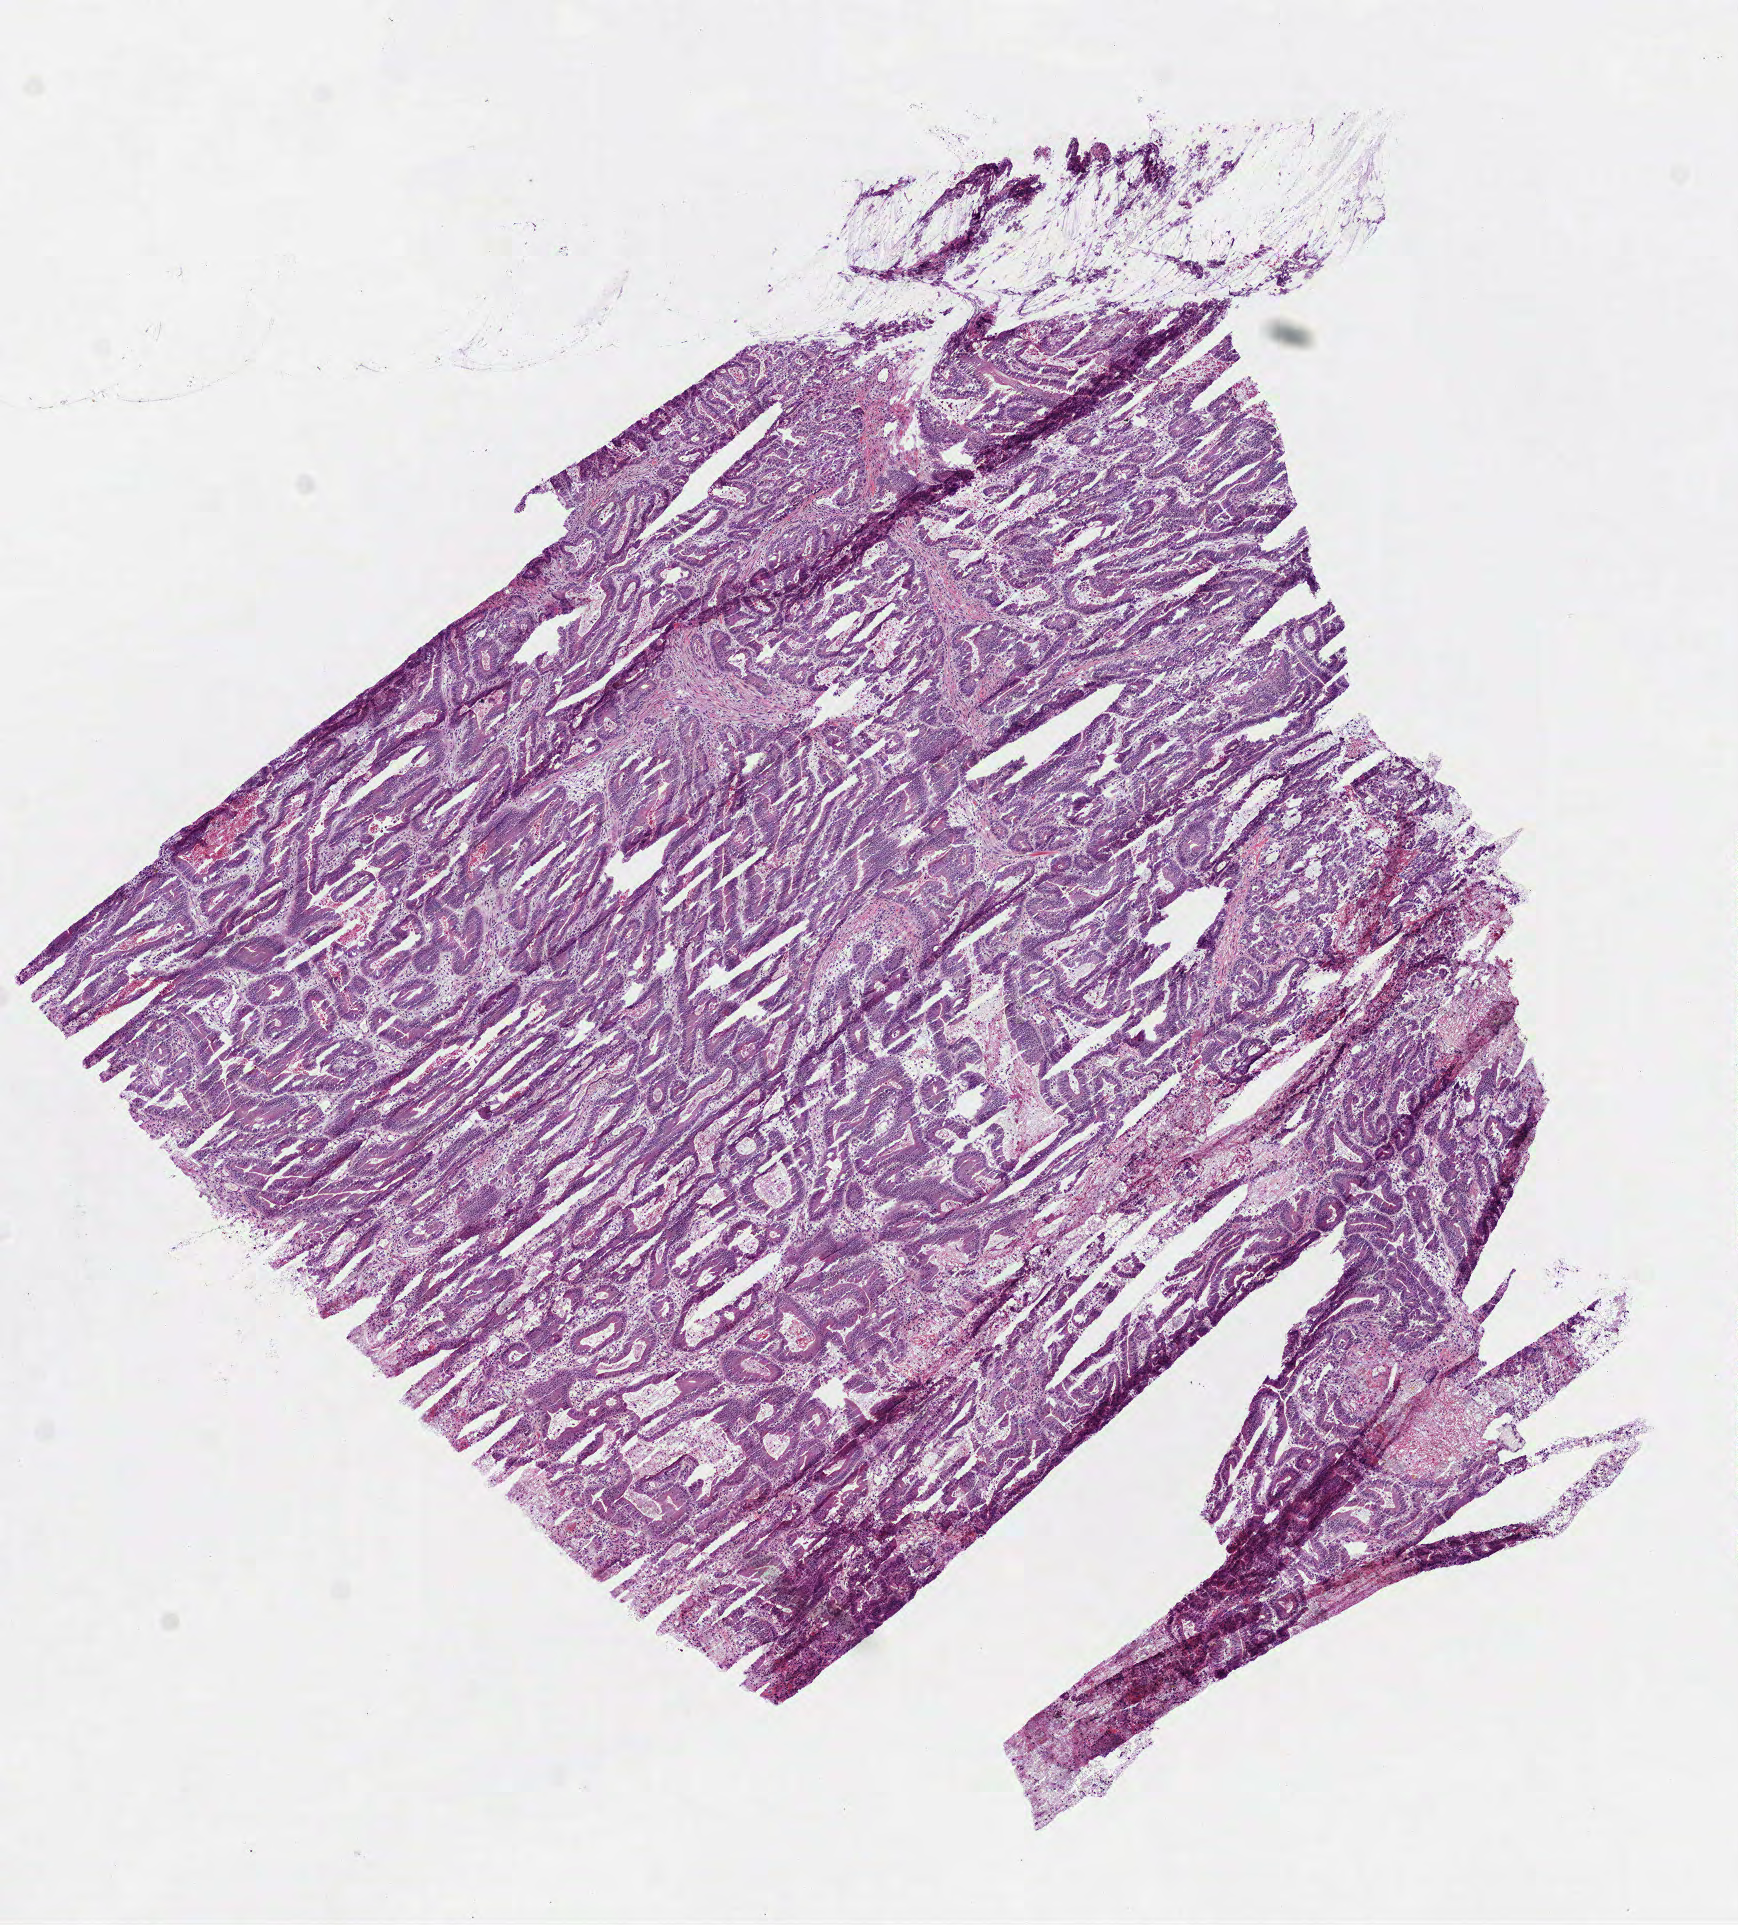
Whole-slide histology image, H&E-stained, low-resolution overview of the scanned area, about 7.0 x 7.8 mm (from a 40x scan); frozen section from the top of the tissue portion; colon, primary tumour sample. Male, age 60 years at initial diagnosis. Slide review estimates, as recorded: tumour cells 85%, tumour nuclei 80%, normal cells 0%, stromal cells 15%, necrosis 0%.
* TNM: T3 N0
* AJCC pathologic stage: IIA
* lymph nodes positive (case pathology): 0 of 16 examined
* pathologic diagnosis: Adenocarcinoma, NOS (ascending colon)